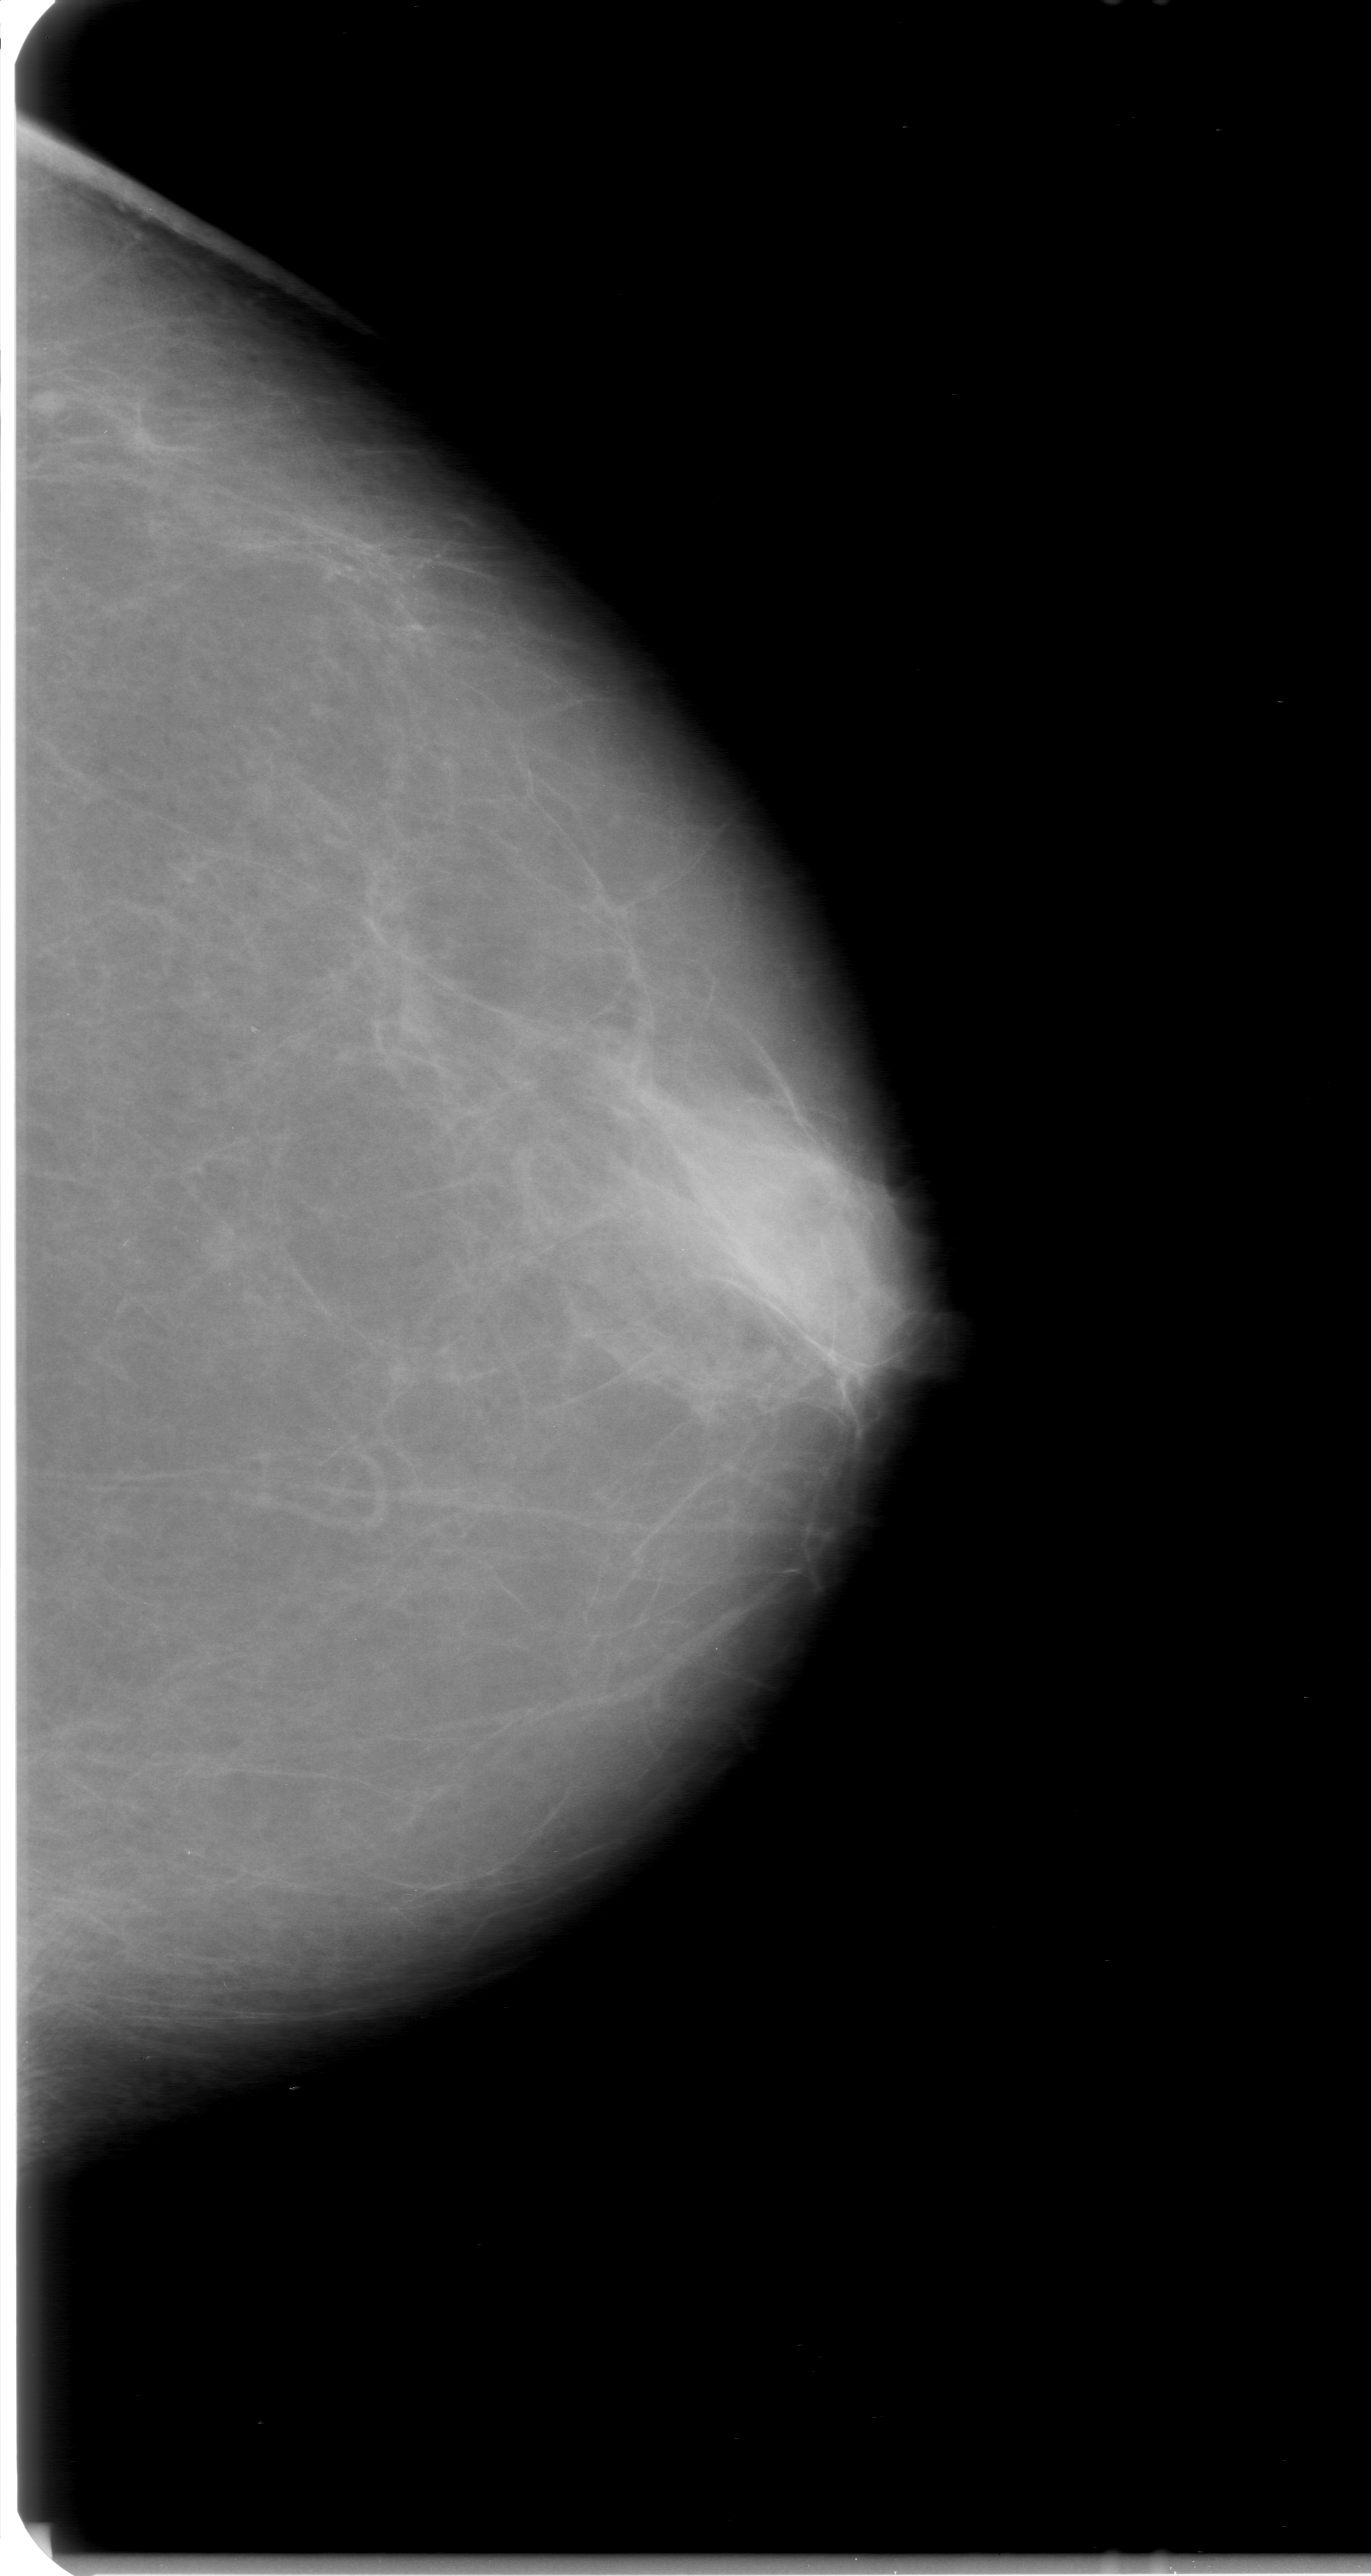
Mammogram (digitized film), left breast, CC view.
Abnormality record for this image: calcifications, morphology fine linear branching, distribution clustered; BI-RADS assessment category 0 (incomplete: needs additional imaging); subtlety rating 4 on a 1 (subtle) to 5 (obvious) scale; pathology result (as recorded, not read from the image): malignant.